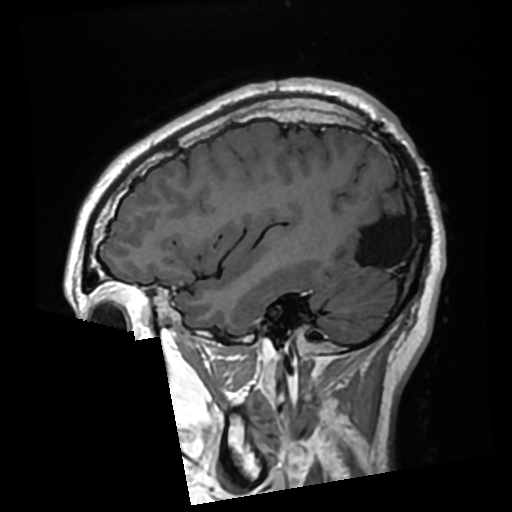
Brain MRI from a brain-tumour surgery series, one sagittal slice; position 84 of 276 along the scan axis; T1-weighted post-contrast; 0.7 mm slice thickness; 512 × 512 image matrix, field of view 250 × 250 mm. From the clinical record (not read from this slice): histopathology: Glioma with ependymal features; WHO grade: 2; tumour location: Left Parietal.
Outlined on this slice (expert manual segmentation):
- previous resection cavity: box from (x=344, y=184) to (x=406, y=266) px